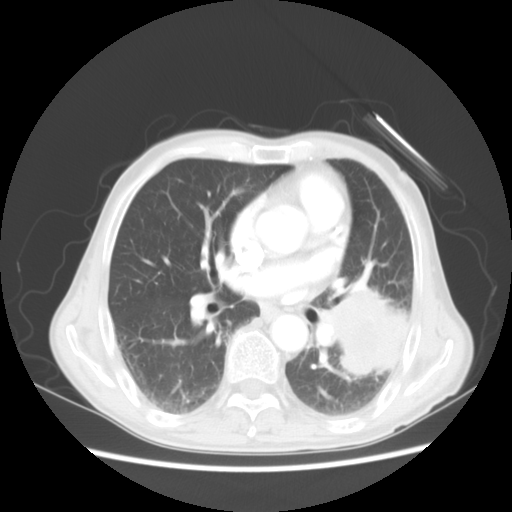
Chest CT, one axial slice. Position 25 of 51 along the scan axis. Reconstruction kernel STANDARD. 120 kVp. Lung window (W 1500 / L -600 HU). 5 mm slice thickness. 512 × 512 image matrix. Patient: male, 64 years. From the clinical record (not read from this slice): clinical TNM (as recorded): T4 N0 M0; histopathological grade: G2-3.
Structures marked on this image (bounding box drawn by a radiologist):
- lung tumour (recorded histology: squamous cell carcinoma): bounding box <318,274,417,397> (left, top, right, bottom; pixels)